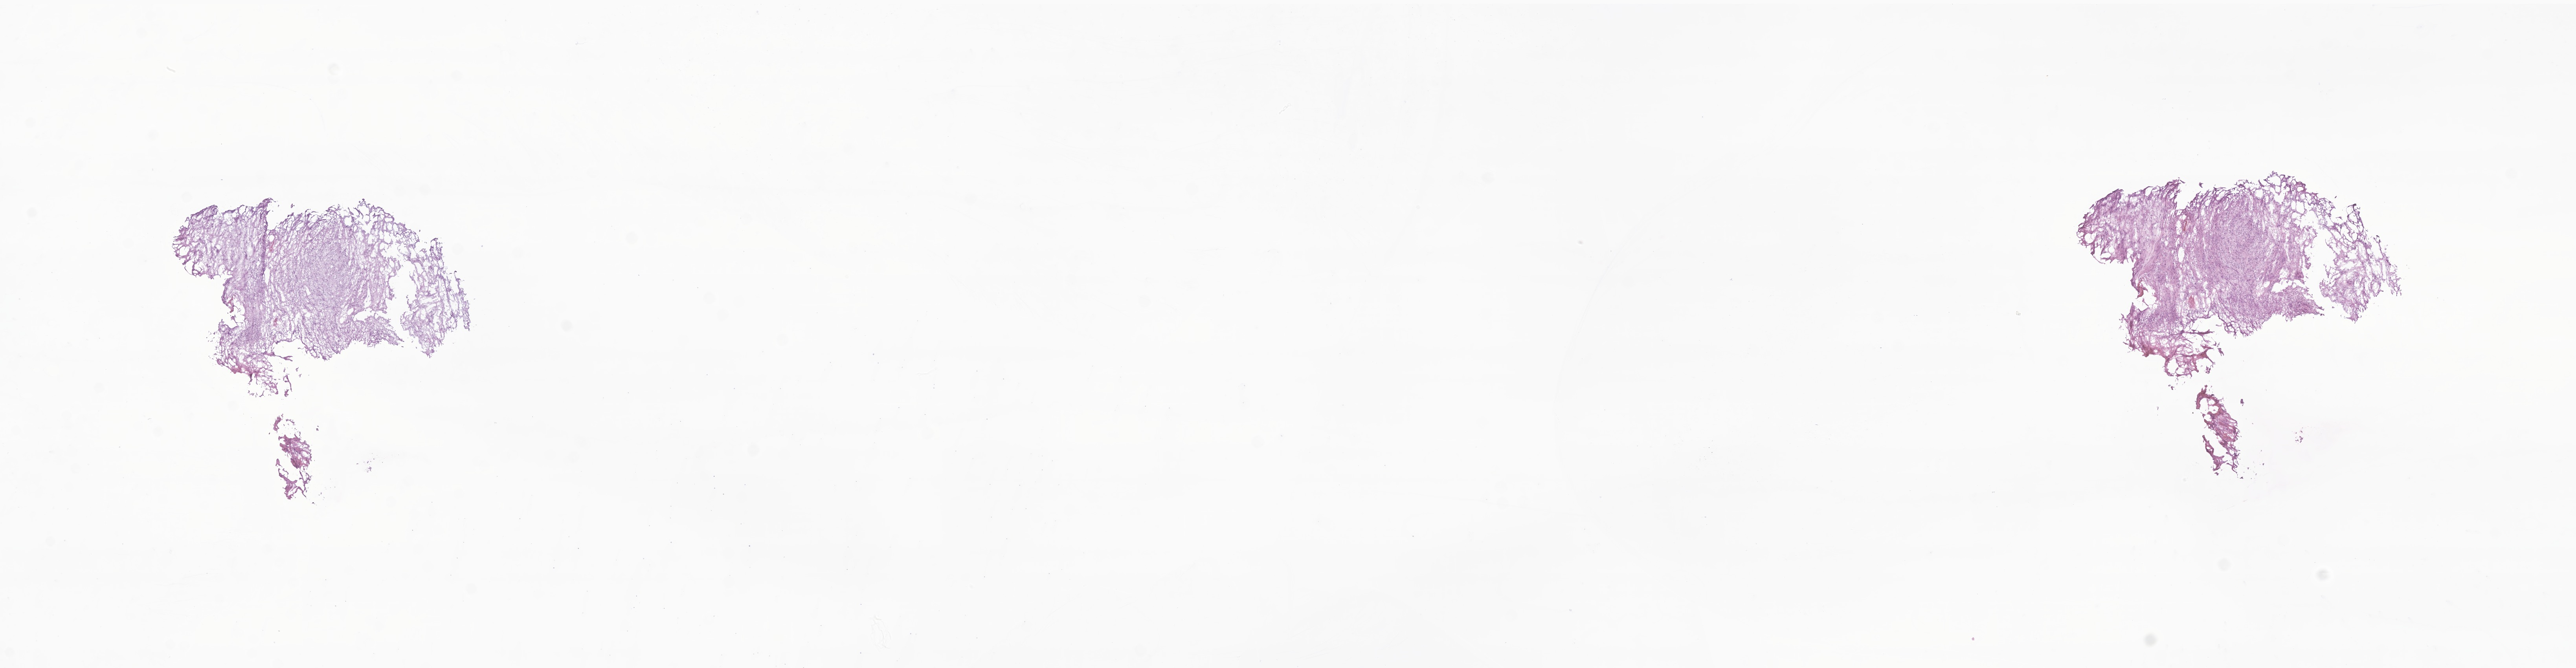
Haematoxylin and eosin whole-slide image of tumor tissue from the brain, low-resolution overview of the scanned area, about 27.6 x 7.2 mm, frozen section. Patient: male, age 193 months.
Recorded diagnosis: Schwannoma, NOS.